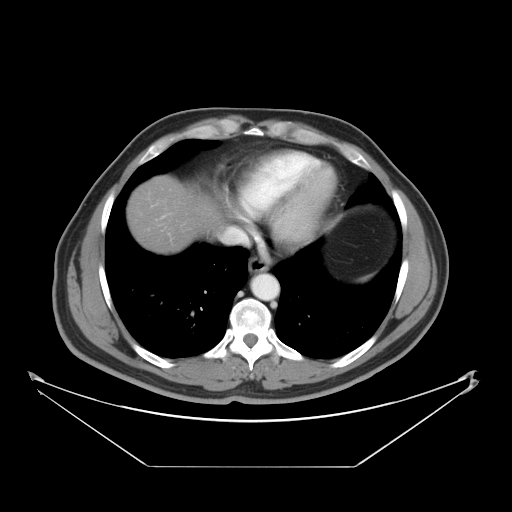
Contrast-enhanced abdominal CT, one axial slice; position 41 of 46 along the scan axis; reconstruction kernel STANDARD; 120 kVp; soft-tissue window (W 400 / L 40 HU); 5 mm slice thickness; 512 × 512 image matrix. Male patient, age 57 years. Case-level facts recorded for this patient, not image findings: diagnosis: colorectal cancer liver metastases, imaged before liver resection; multiple liver metastases: no; largest metastasis: 3.3 cm; disease in both lobes: no.
Annotated regions visible in this slice (manually delineated by an expert):
- liver: bounding box [x1, y1, x2, y2] px = [128, 178, 220, 253]
- planned liver remnant (the part of the liver to remain after resection): [128, 178, 220, 253]